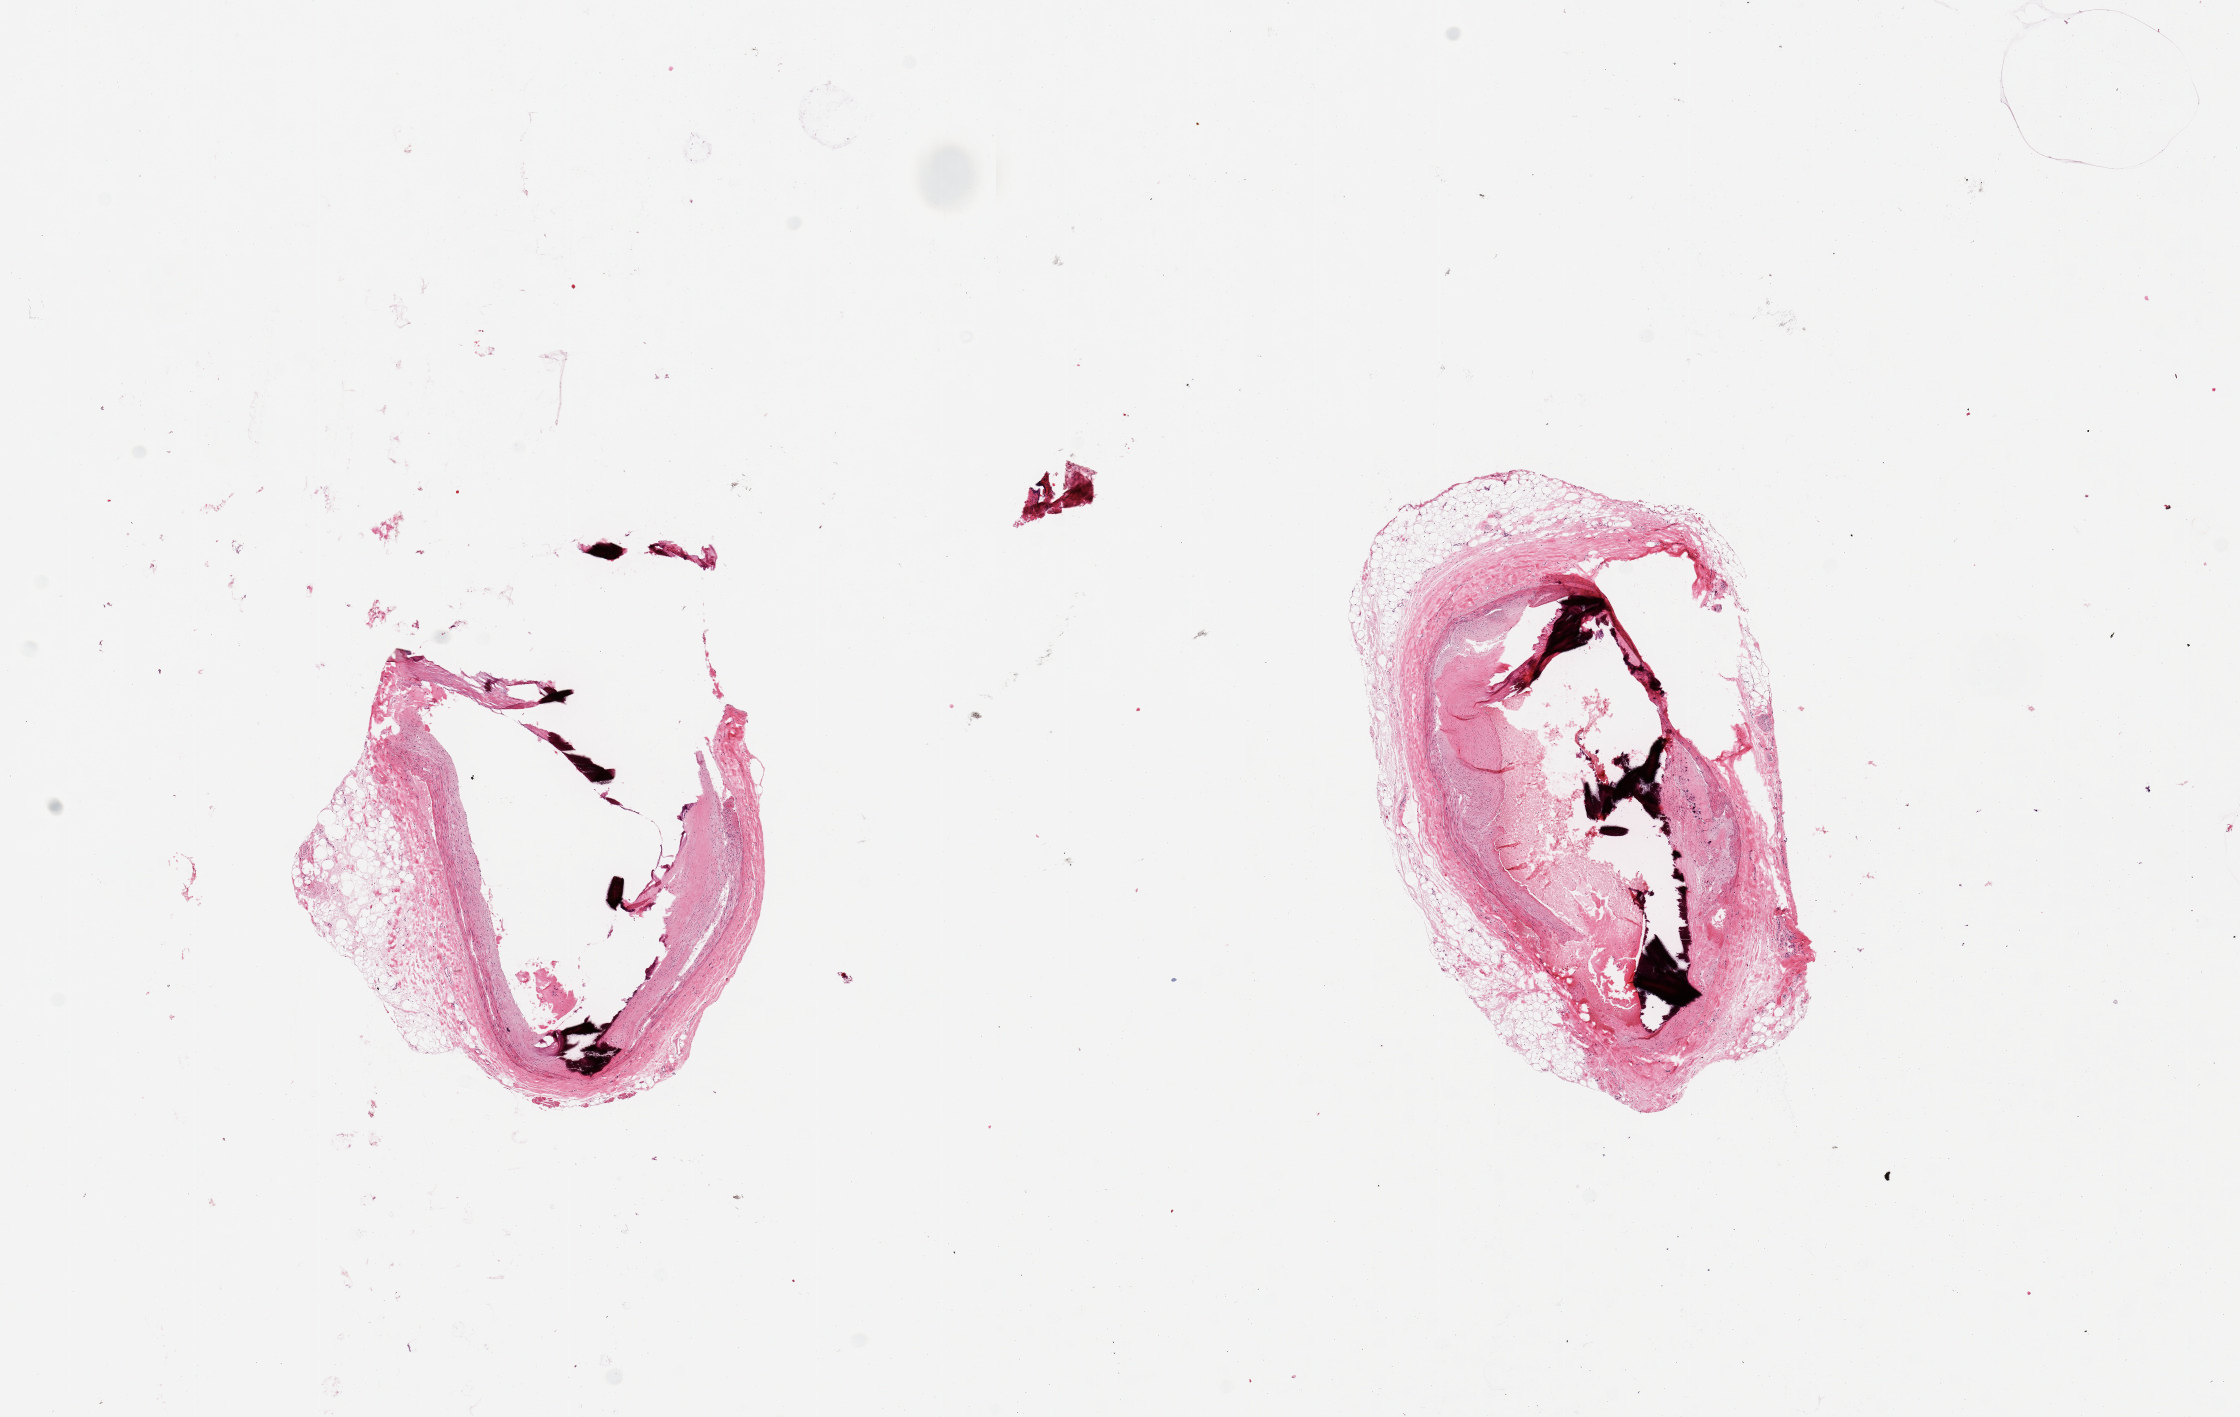
Whole-slide image, hematoxylin and eosin (H&E) stain, brightfield — low-resolution overview of the scanned area, about 17.7 x 11.2 mm (from a 20x scan); PAXgene-fixed, paraffin-embedded tissue; section of coronary artery (target tissue); tissue donor sample. Male donor.
Pathologist's review note for this sample: 2 pieces, subtotally occlusive, calcified atherosis; adherent fat up to ~1mm.